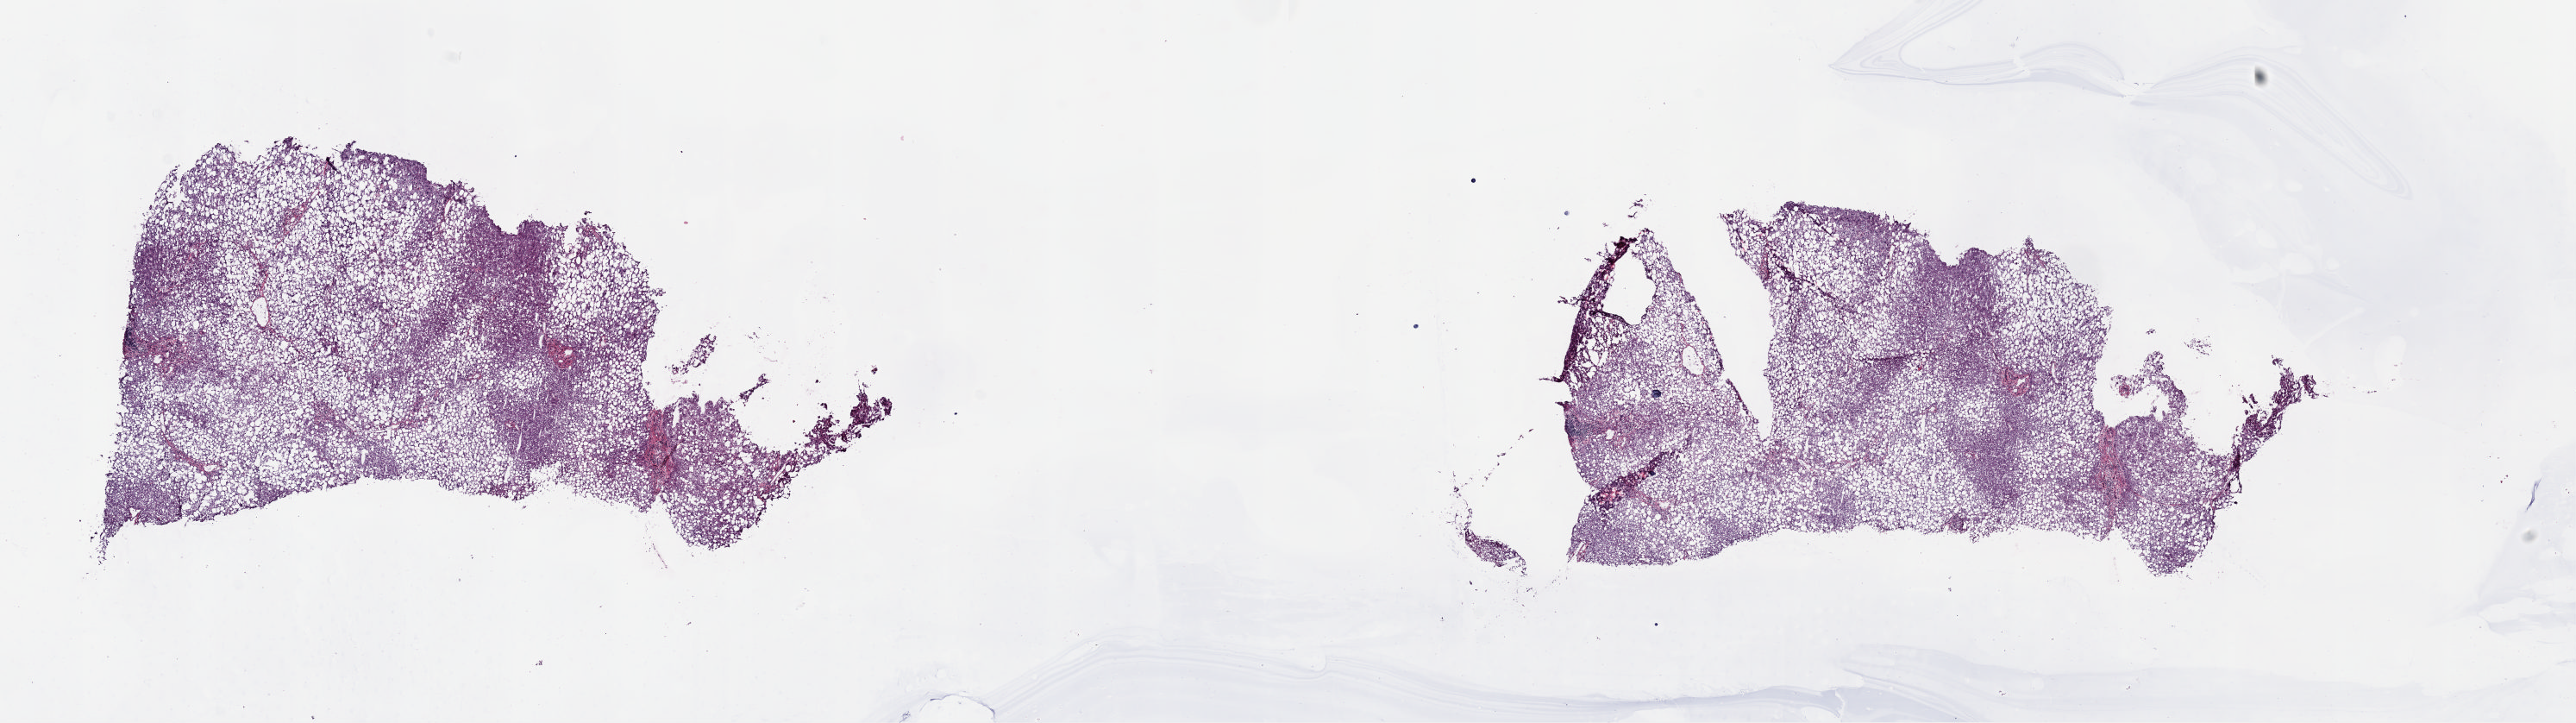
Hematoxylin and eosin (H&E) stained whole-slide image, whole scanned area (about 23.6 x 6.6 mm) shown as a low-resolution overview, frozen section from the top of the tissue portion, solid tissue normal (non-tumour tissue) sample from the liver. Male, age 61 years at initial diagnosis. Slide review estimates, as recorded: tumour cells 0%, tumour nuclei 0%, normal cells 100%, stromal cells 0%, necrosis 0%. Infiltration values recorded for this section: lymphocyte infiltration 3%, monocyte infiltration 0%, neutrophil infiltration 0%.
* this section: solid tissue normal sample (biorepository sample class)
* patient diagnosis: Hepatocellular carcinoma, NOS